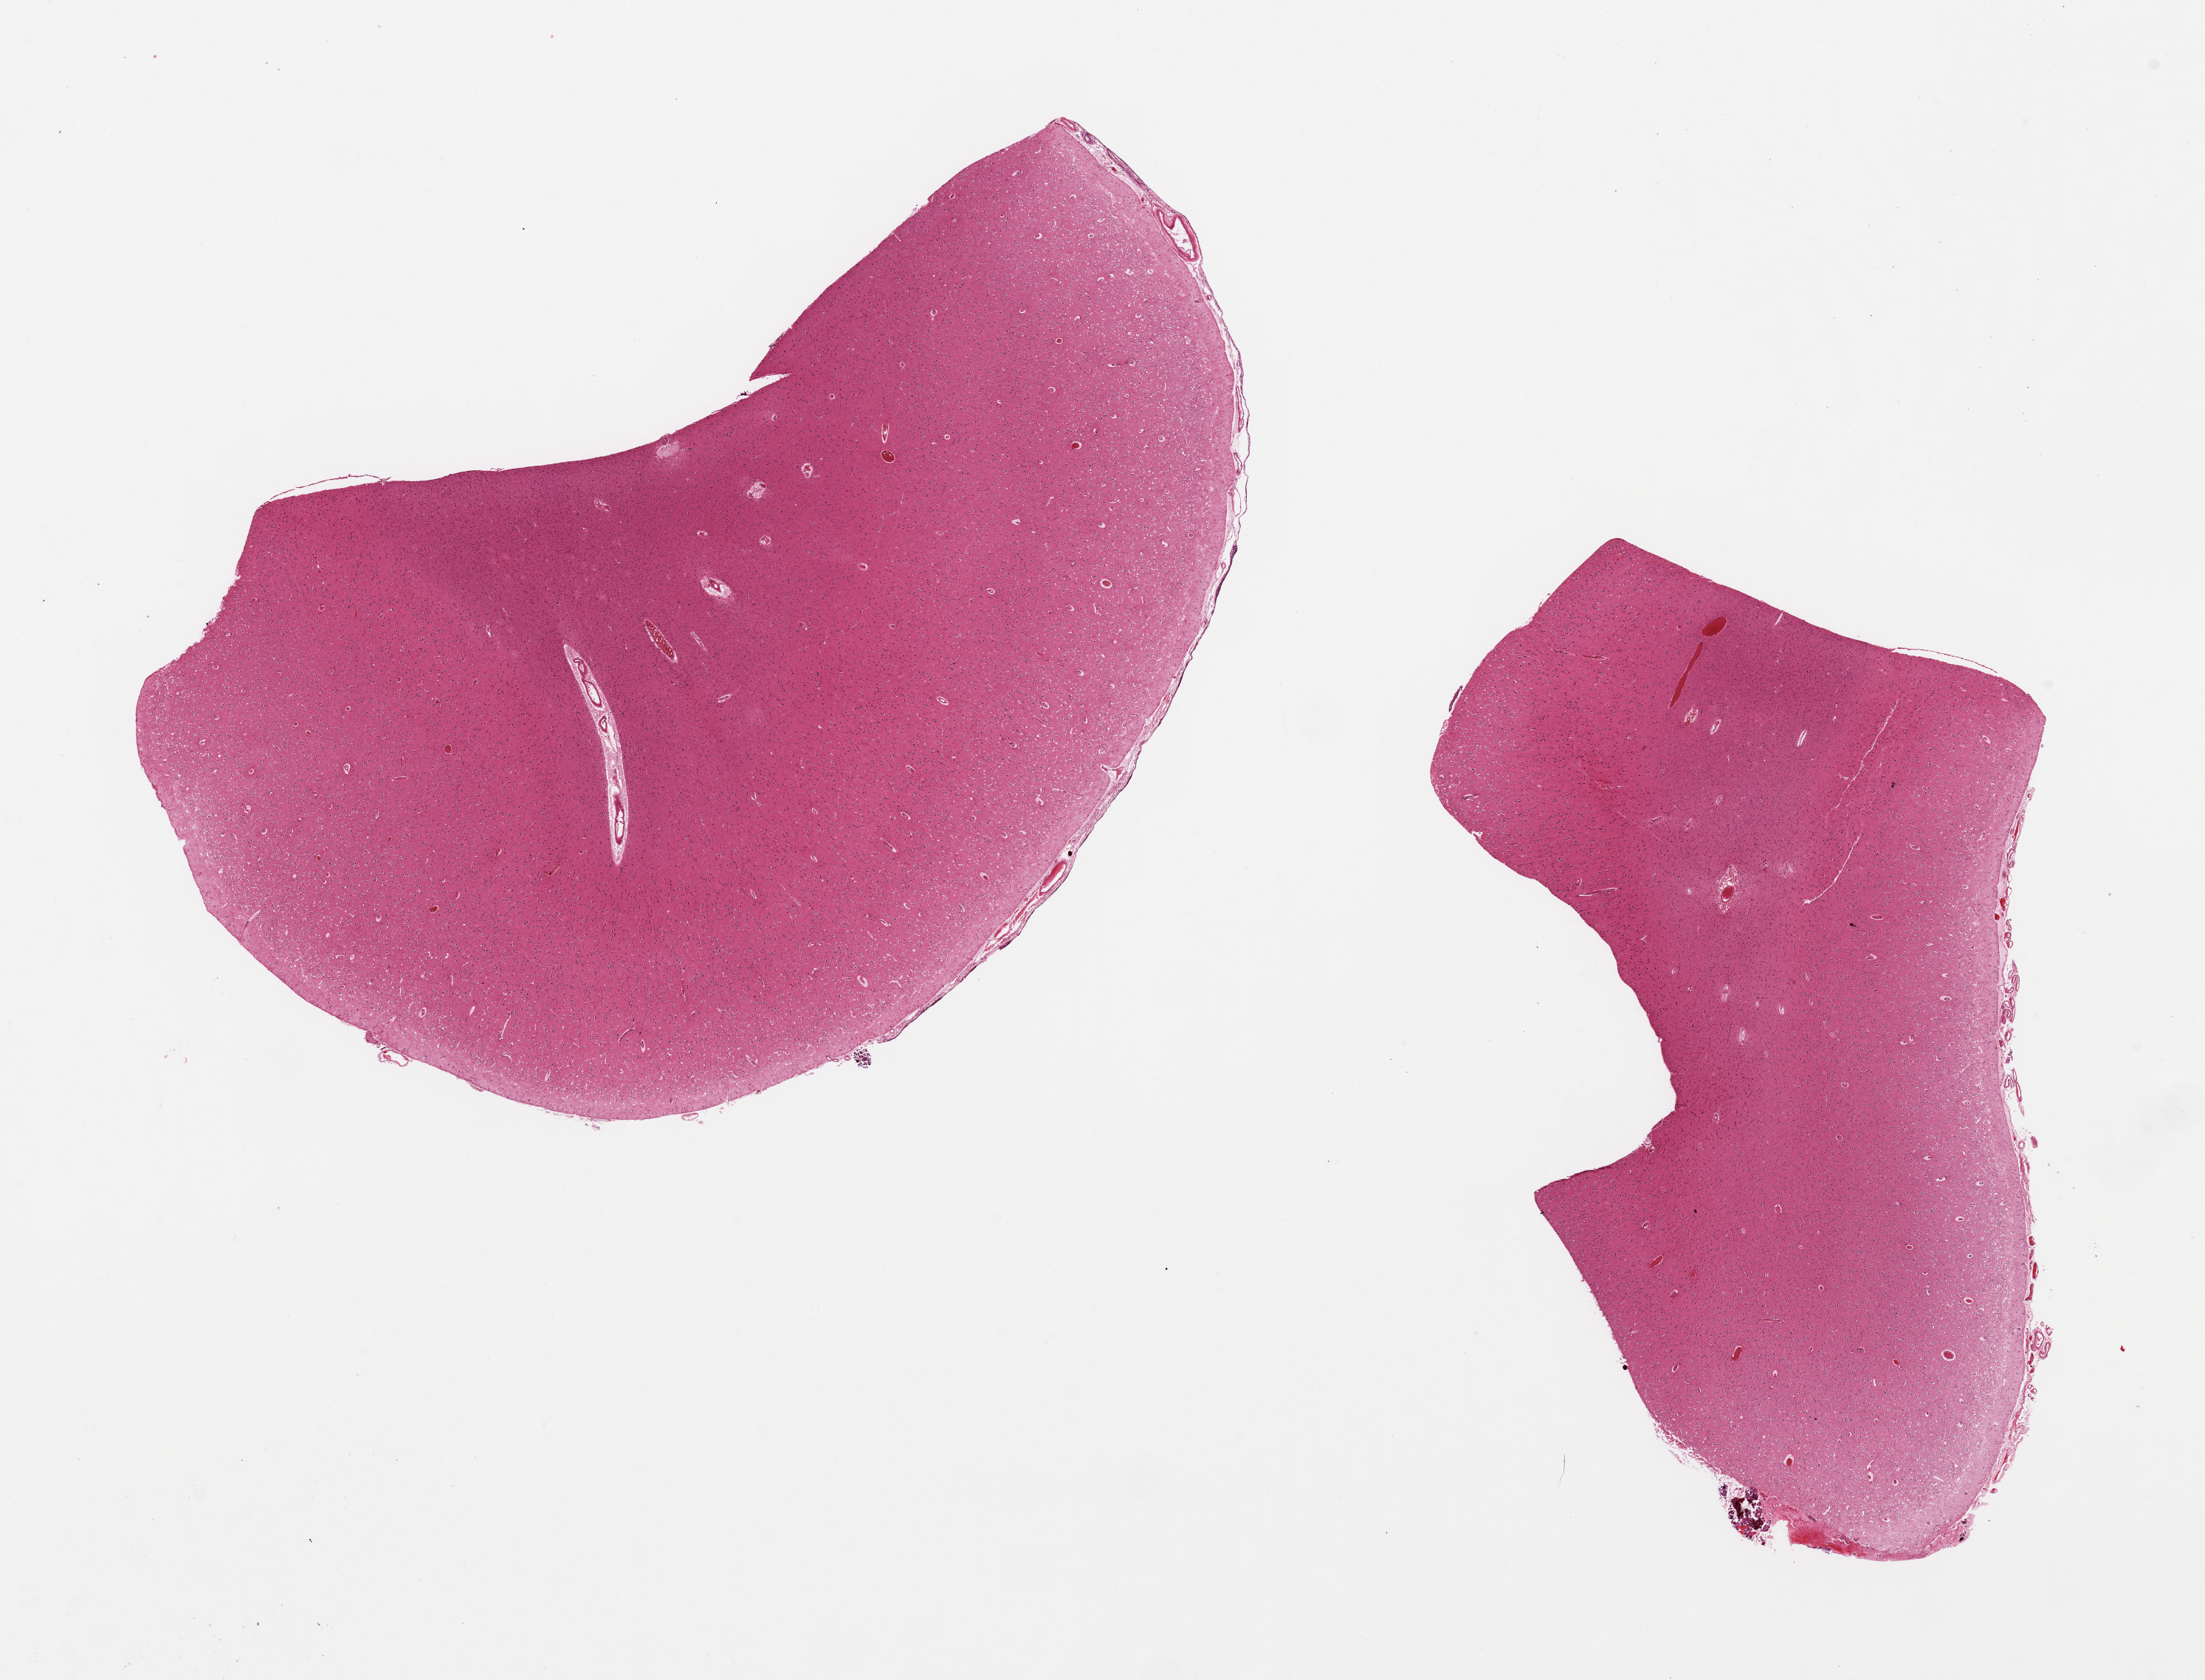
Haematoxylin and eosin whole-slide image, shown as a low-resolution overview of the whole scanned area (about 23.6 x 18.0 mm, acquisition: 20x scan); PAXgene-fixed paraffin-embedded (PFPE) section; section of cerebral cortex (target tissue); tissue donor sample.
Review note (as recorded): 2 pieces.